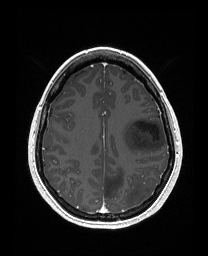
Brain MRI from a brain-tumour surgery series, one axial slice; position 113 of 176 along the scan axis; T1-weighted post-contrast; 208 × 256 image matrix, field of view 203 × 250 mm. From the clinical record (not read from this slice): histopathology: Astrocytoma; WHO grade: 3; IDH mutation: yes; tumour location: Left Frontal.
Structures marked on this image (expert manual segmentation):
- tumour: bounding box [x1, y1, x2, y2] px = [121, 118, 166, 154]